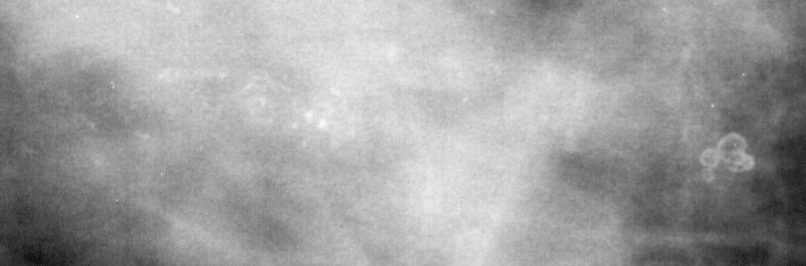
Crop from a digitized film mammogram around one marked abnormality, left breast, CC view, BI-RADS breast density category 3 (scale 1–4).
Finding: calcifications, morphology pleomorphic, distribution clustered; BI-RADS assessment category 4; subtlety rating 2 on a 1 (subtle) to 5 (obvious) scale; pathology result (as recorded, not read from the image): malignant.